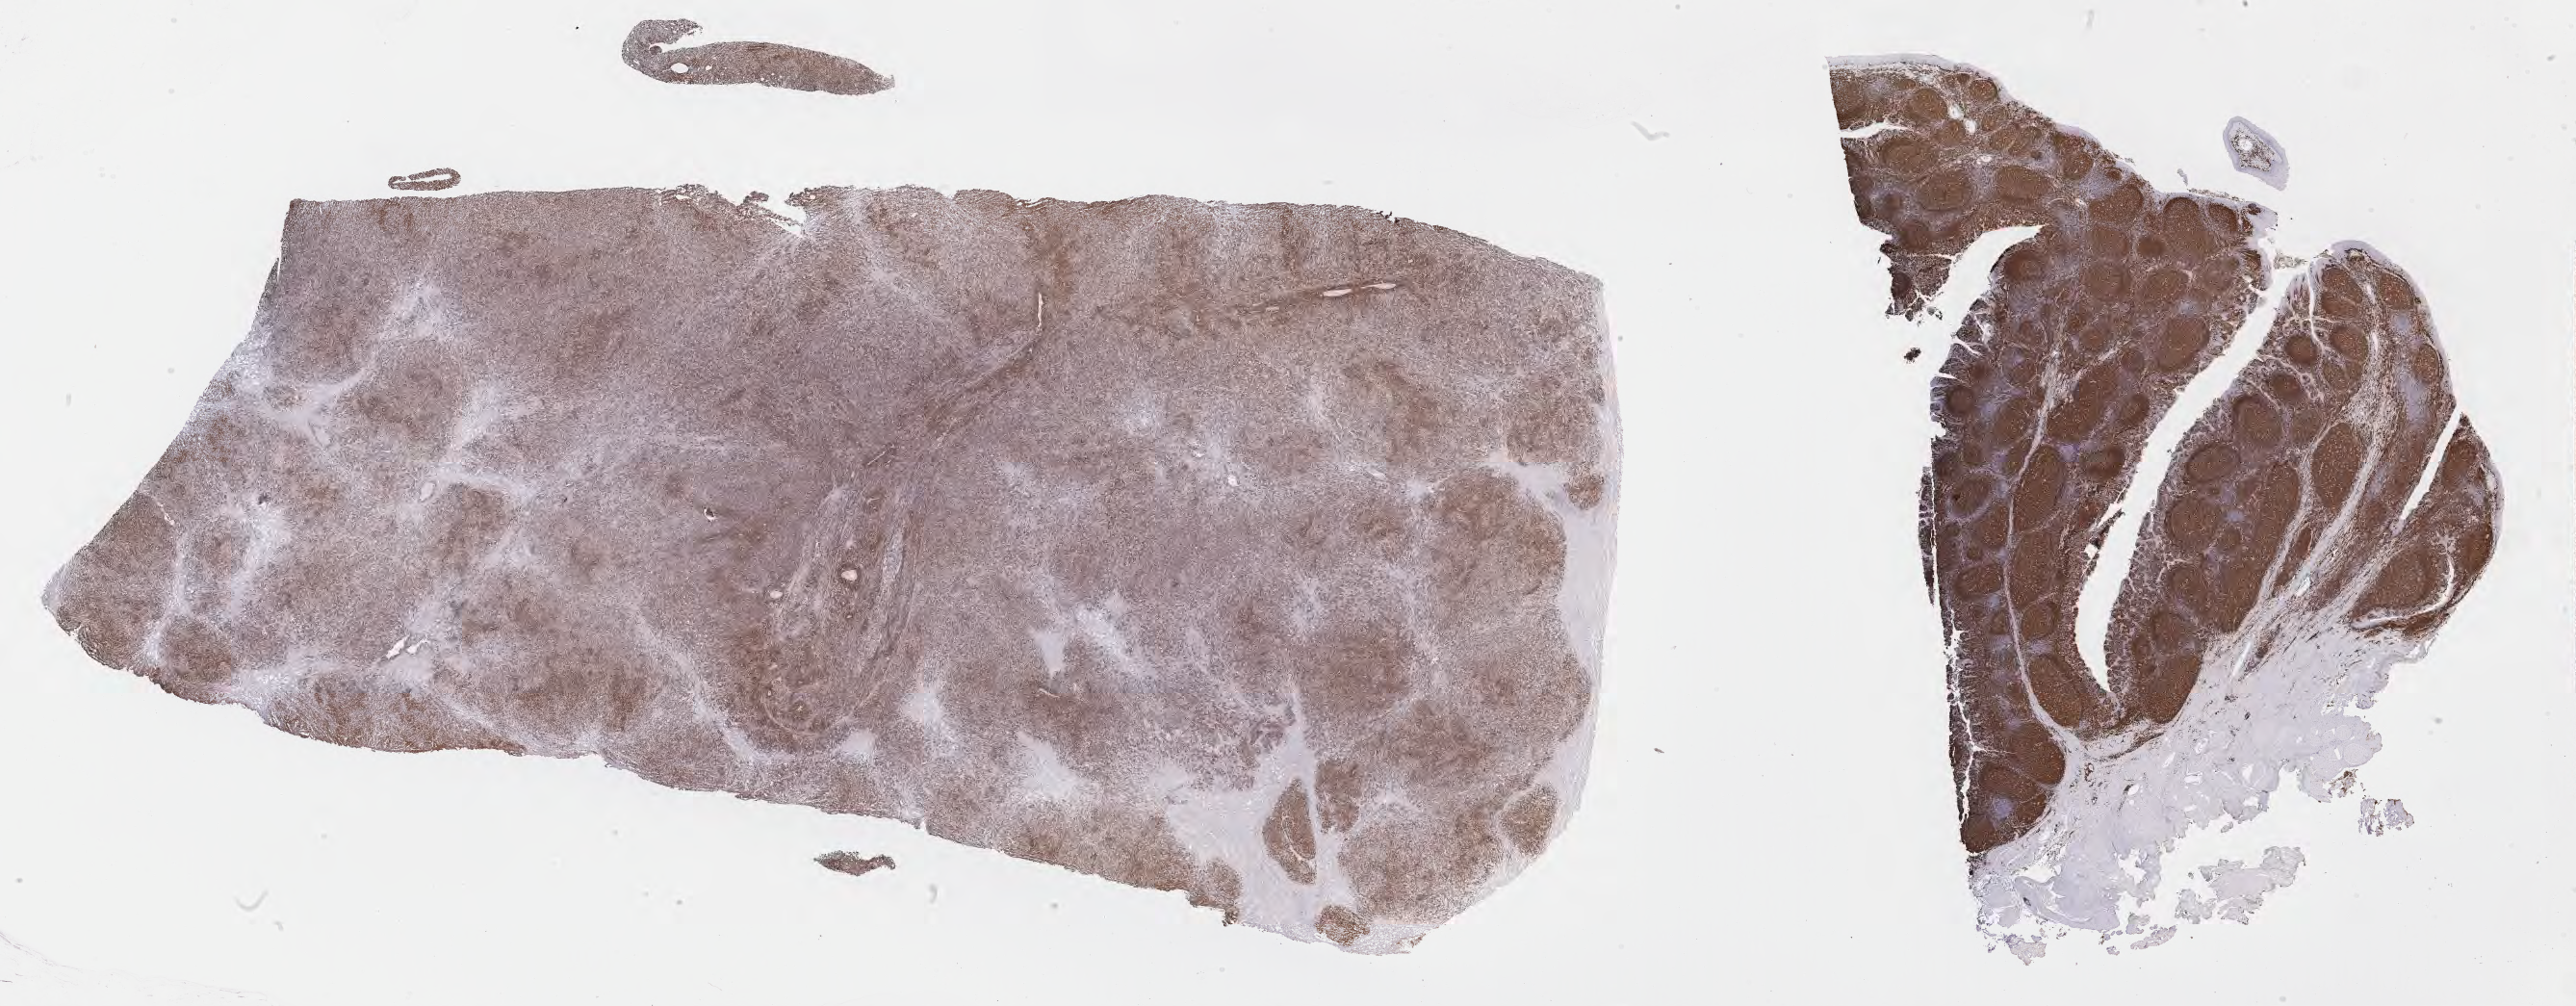
Immunohistochemistry (IHC) whole-slide image stained for CD79a — low-resolution overview of the scanned area, about 43.3 x 16.9 mm; specimen: tumor tissue. Patient male; age 39 years.
Diagnosis: Diffuse large B-cell lymphoma, NOS.